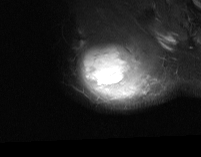
MRI of an extremity soft-tissue mass, one axial slice. Slice 56 of 74 in the series (ordered by position). STIR. MR volume resampled by the dataset authors to the PET/CT grid (not the native acquisition matrix). 3.27 mm slice thickness. 201 × 157 image matrix, field of view 196 × 153 mm. Male patient. Case-level facts recorded for this patient, not image findings: histological type: pleiomorphic spindle cell undifferentiated; grade: high; site of the primary tumour: right parascapusular.
Outlined on this slice (expert contour drawn on MRI and transferred to this co-registered scan by the dataset authors):
- gross tumour volume including surrounding oedema: bounding box (x1, y1, x2, y2) in pixels: (79, 39, 164, 101)
- gross tumour volume (mass): (83, 46, 137, 97)